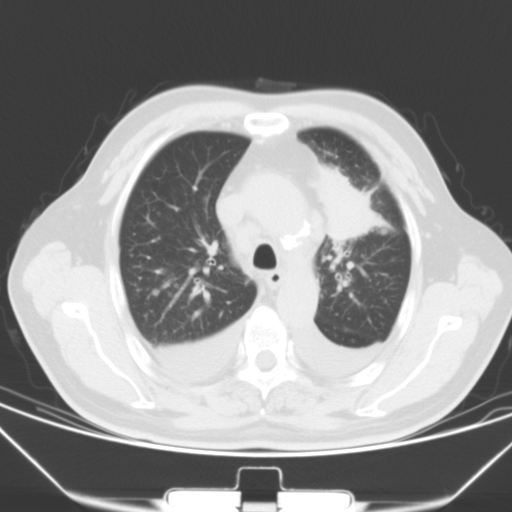
Chest CT, one axial slice. Slice 46 of 66 in the series (ordered by position). Lung window (W 1500 / L -600 HU). 512 × 512 image matrix, field of view 352 × 352 mm. Male patient, age 66 years. Case-level facts recorded for this patient, not image findings: clinical TNM (as recorded): T1c N0 M0.
Outlined on this slice (bounding box drawn by a radiologist):
- lung tumour (recorded histology: adenocarcinoma): bounding box [x1, y1, x2, y2] px = [308, 156, 381, 245]